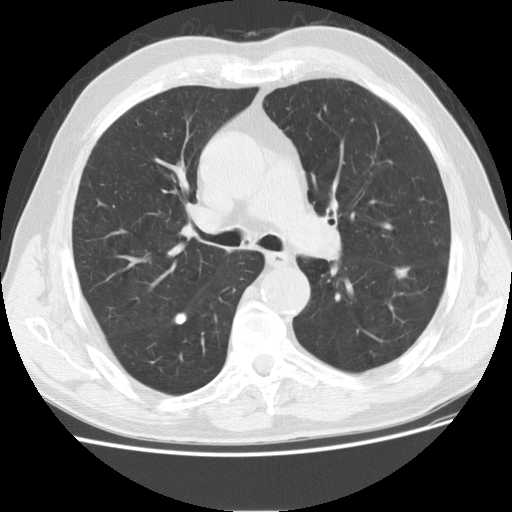
Axial slice from a low-dose chest CT screening exam. Second annual screen. Lung window (W 1500 / L -600 HU). 2.5 mm slice thickness. Standard (soft-tissue) reconstruction kernel (STANDARD). Male, age 73 years at enrolment. Current smoker at enrolment.
• Lesion marked by an expert reader, bounding box (x1, y1, x2, y2) in pixels: (372, 256, 422, 297).
• The exam's reader record, not a measurement of the box and not confirmed to be the same lesion: non-calcified nodule or mass ≥4 mm, left lower lobe, 16 × 10 mm, smooth margins, soft tissue attenuation, pre-existing on the prior screen: yes; interval growth: yes.
• Participant outcome: lung cancer diagnosed 76 days after this screen — adenocarcinoma, NOS, left lower lobe, poorly differentiated (G3), stage IIA (AJCC 6th edition), 12 mm at pathology.